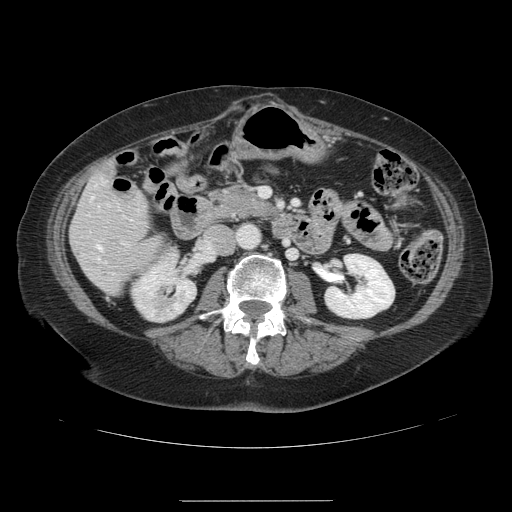
Contrast-enhanced abdominal CT, one axial slice. Intravenous contrast given. Soft-tissue window (W 400 / L 40 HU). 512 × 512 image matrix, field of view 393 × 393 mm. Female patient, age 74 years. Case-level facts recorded for this patient, not image findings: diagnosis: colorectal cancer liver metastases, imaged before liver resection; multiple liver metastases: yes; largest metastasis: 7 cm; disease in both lobes: yes.
Structures marked on this image (manually delineated by an expert):
- hepatic veins: bounding box [x1, y1, x2, y2] px = [90, 197, 101, 249]
- liver: [71, 174, 160, 294]
- planned liver remnant (the part of the liver to remain after resection): [72, 174, 160, 288]